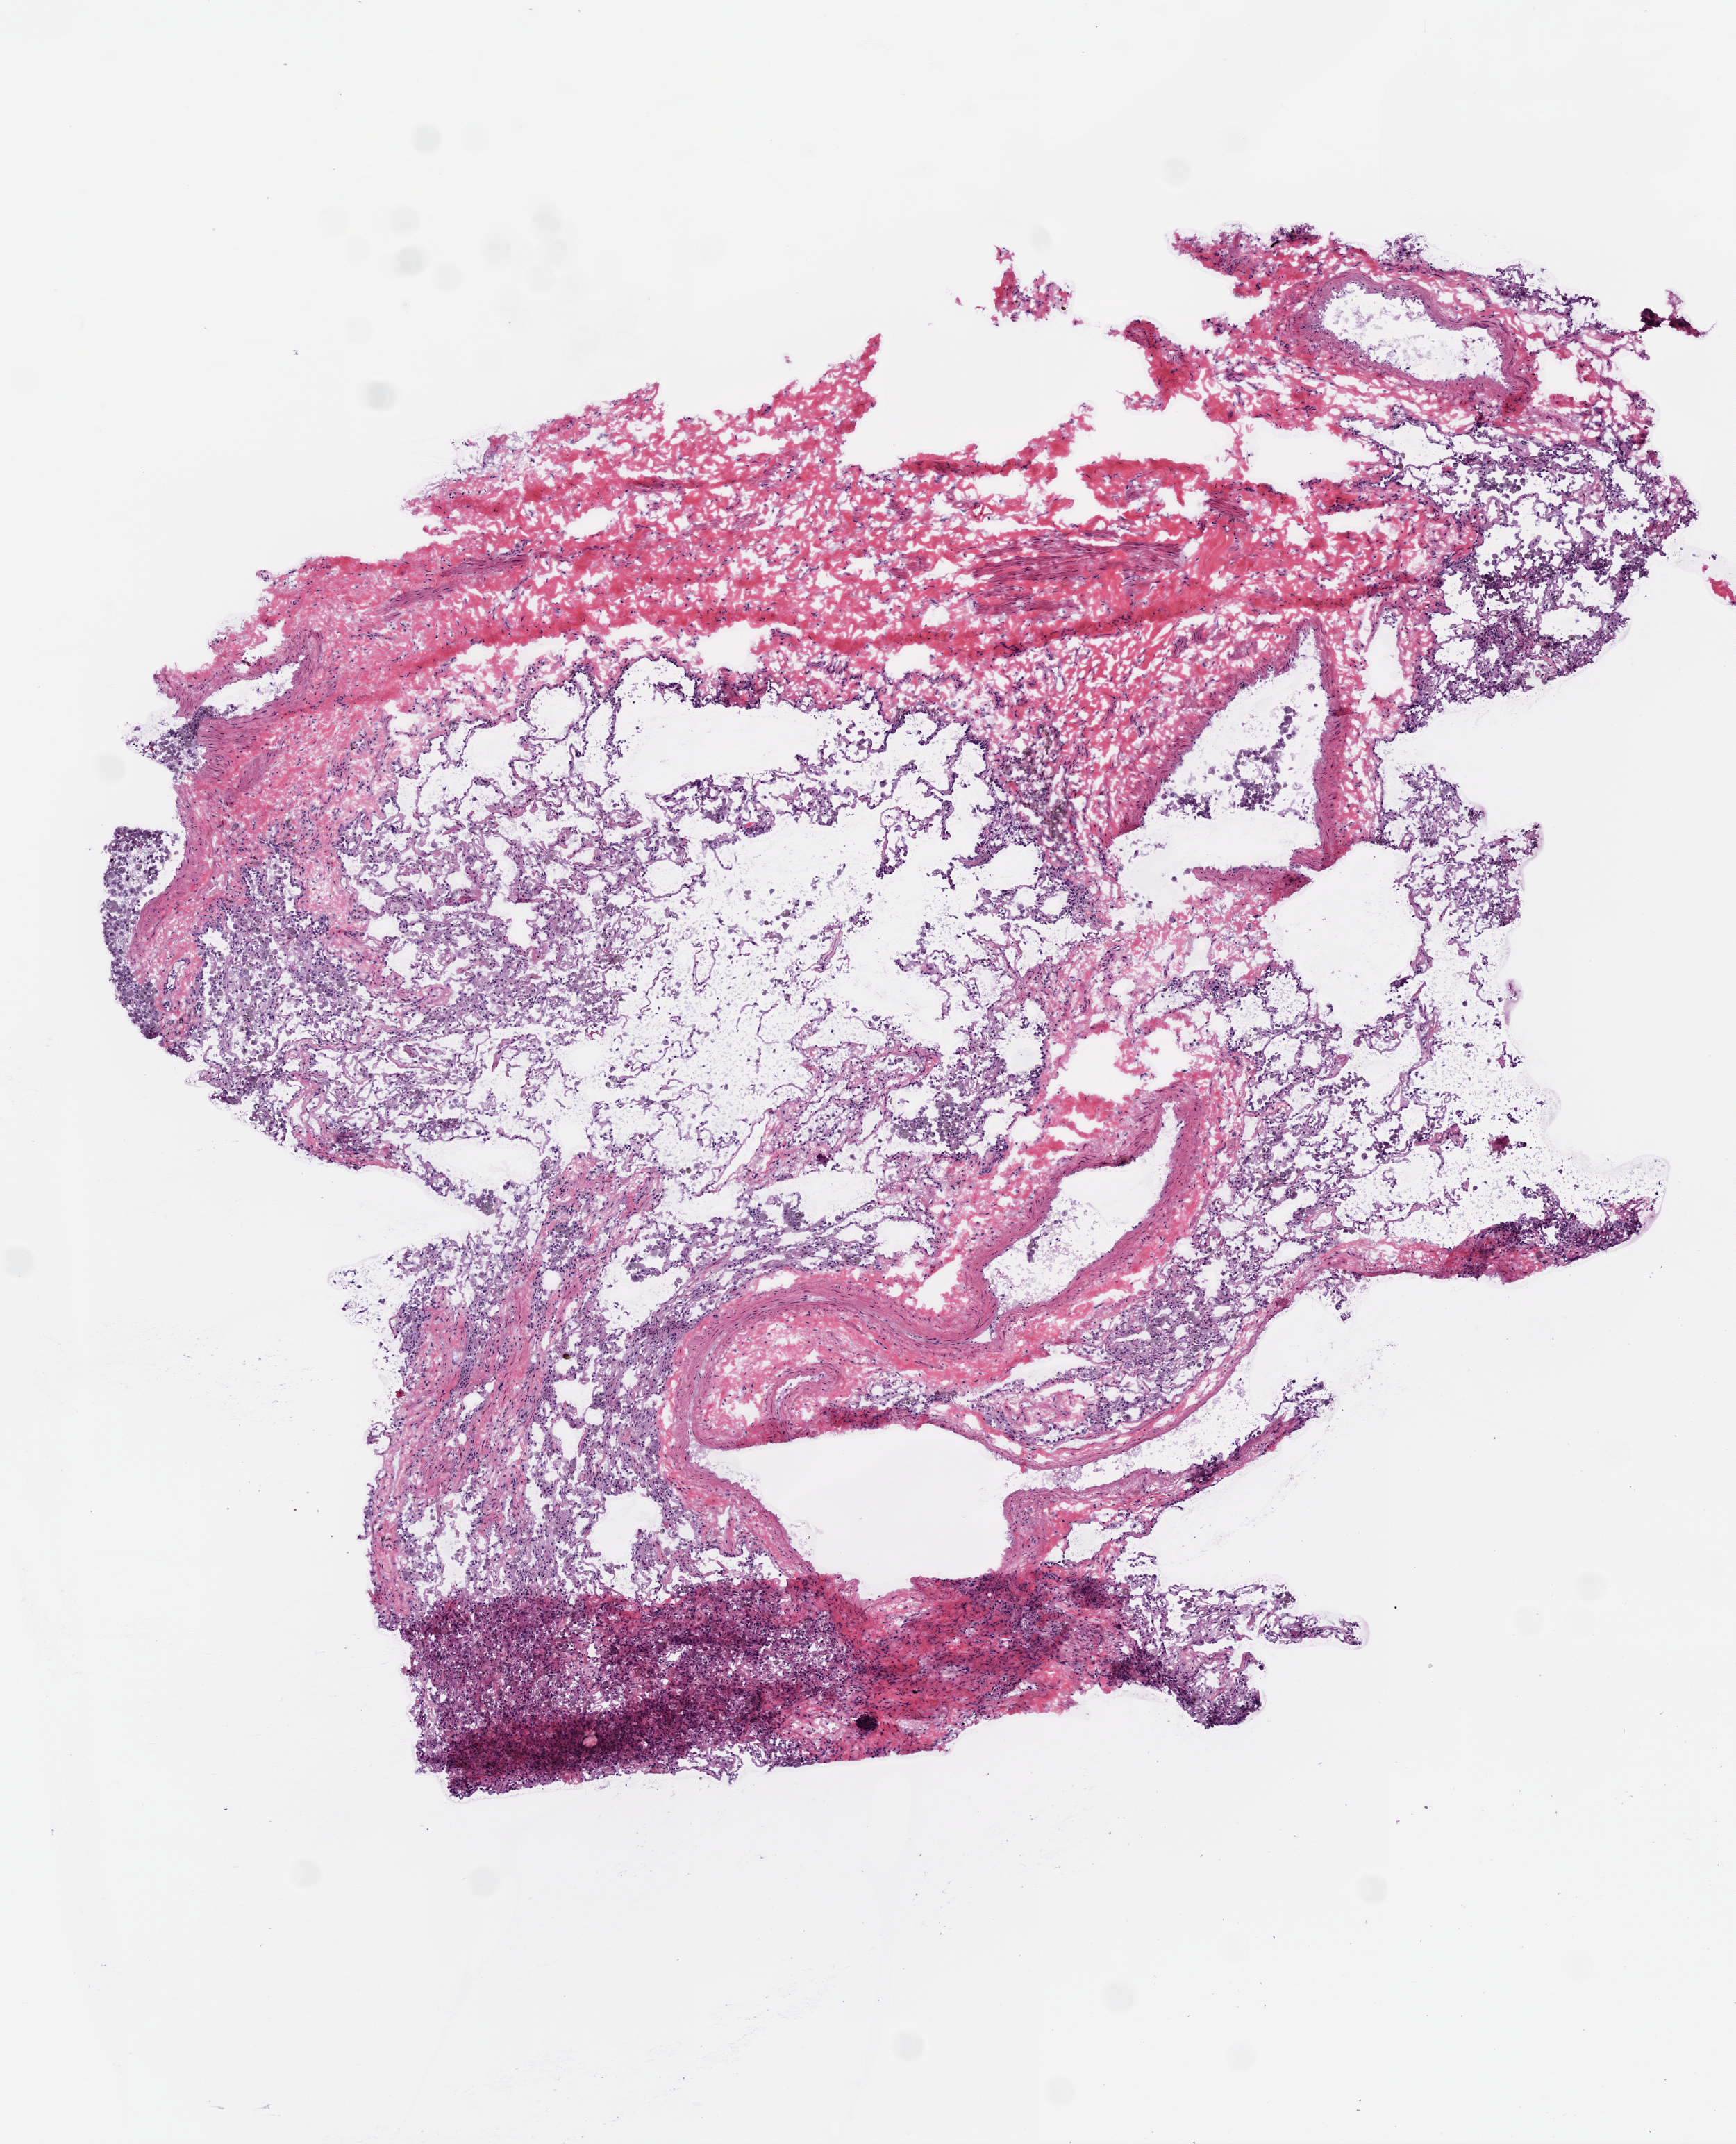
H&E whole-slide image — a low-resolution overview of the entire scanned area, about 5.0 x 6.2 mm (slide scanned at 20x), frozen section from the top of the tissue portion, lung, solid tissue normal (non-tumour tissue) sample. Male patient; age at initial diagnosis 67 years.
- this section: solid tissue normal (non-tumour) sample from the same patient
- patient diagnosis: Squamous cell carcinoma, NOS (upper lobe, lung)